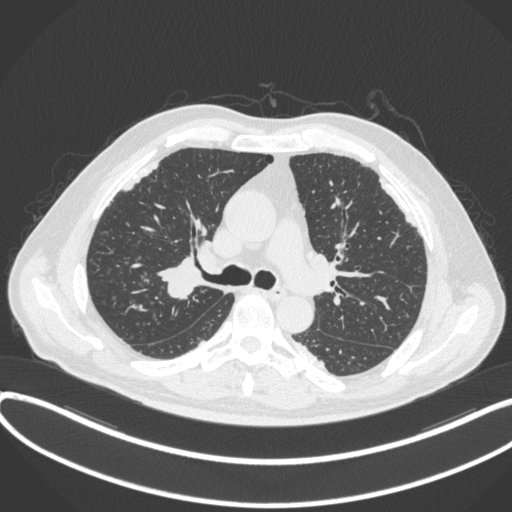
Chest CT, one axial slice; slice 271 of 455 in the series (ordered by position); reconstruction kernel B31f; lung window (W 1500 / L -600 HU); 512 × 512 image matrix. Patient: male, 58 years. Case-level facts recorded for this patient, not image findings: clinical TNM (as recorded): T1c N0 M0.
Structures marked on this image (bounding box drawn by a radiologist):
- lung tumour (recorded histology: squamous cell carcinoma): box from (x=156, y=253) to (x=207, y=305) px